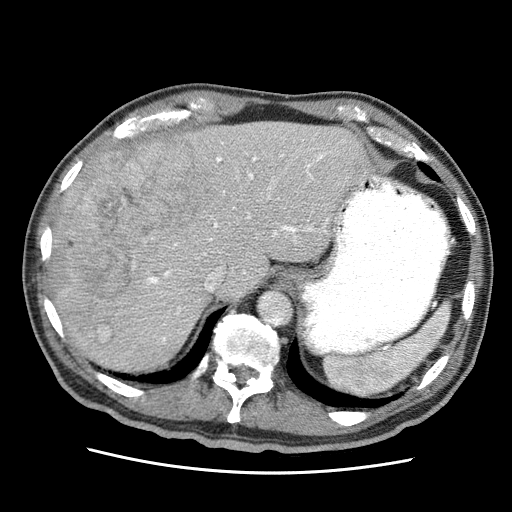
Contrast-enhanced abdominal CT (liver protocol), one axial slice. Position 46 of 75 along the scan axis. Reconstruction kernel STANDARD. 120 kVp. Soft-tissue window (W 400 / L 40 HU). 2.5 mm slice thickness. 512 × 512 image matrix, field of view 360 × 360 mm. From the clinical record (not read from this slice): diagnosis: hepatocellular carcinoma (patient treated with transarterial chemoembolisation; whether this scan precedes or follows treatment is not stated here); TNM stage (as recorded): Stage-IIIA; Child-Pugh class: A; tumour differentiation: well differentiated; tumour nodularity: multinodular.
Structures marked on this image (semi-automatically segmented with operator editing):
- abdominal aorta: bounding box (x1, y1, x2, y2) in pixels: (258, 291, 292, 325)
- liver parenchyma outside the tumour (the mass and vessels are separate outlines, so this box may not span the whole liver): (52, 122, 370, 370)
- mass: (50, 139, 217, 344)
- liver vessels: (133, 133, 348, 343)